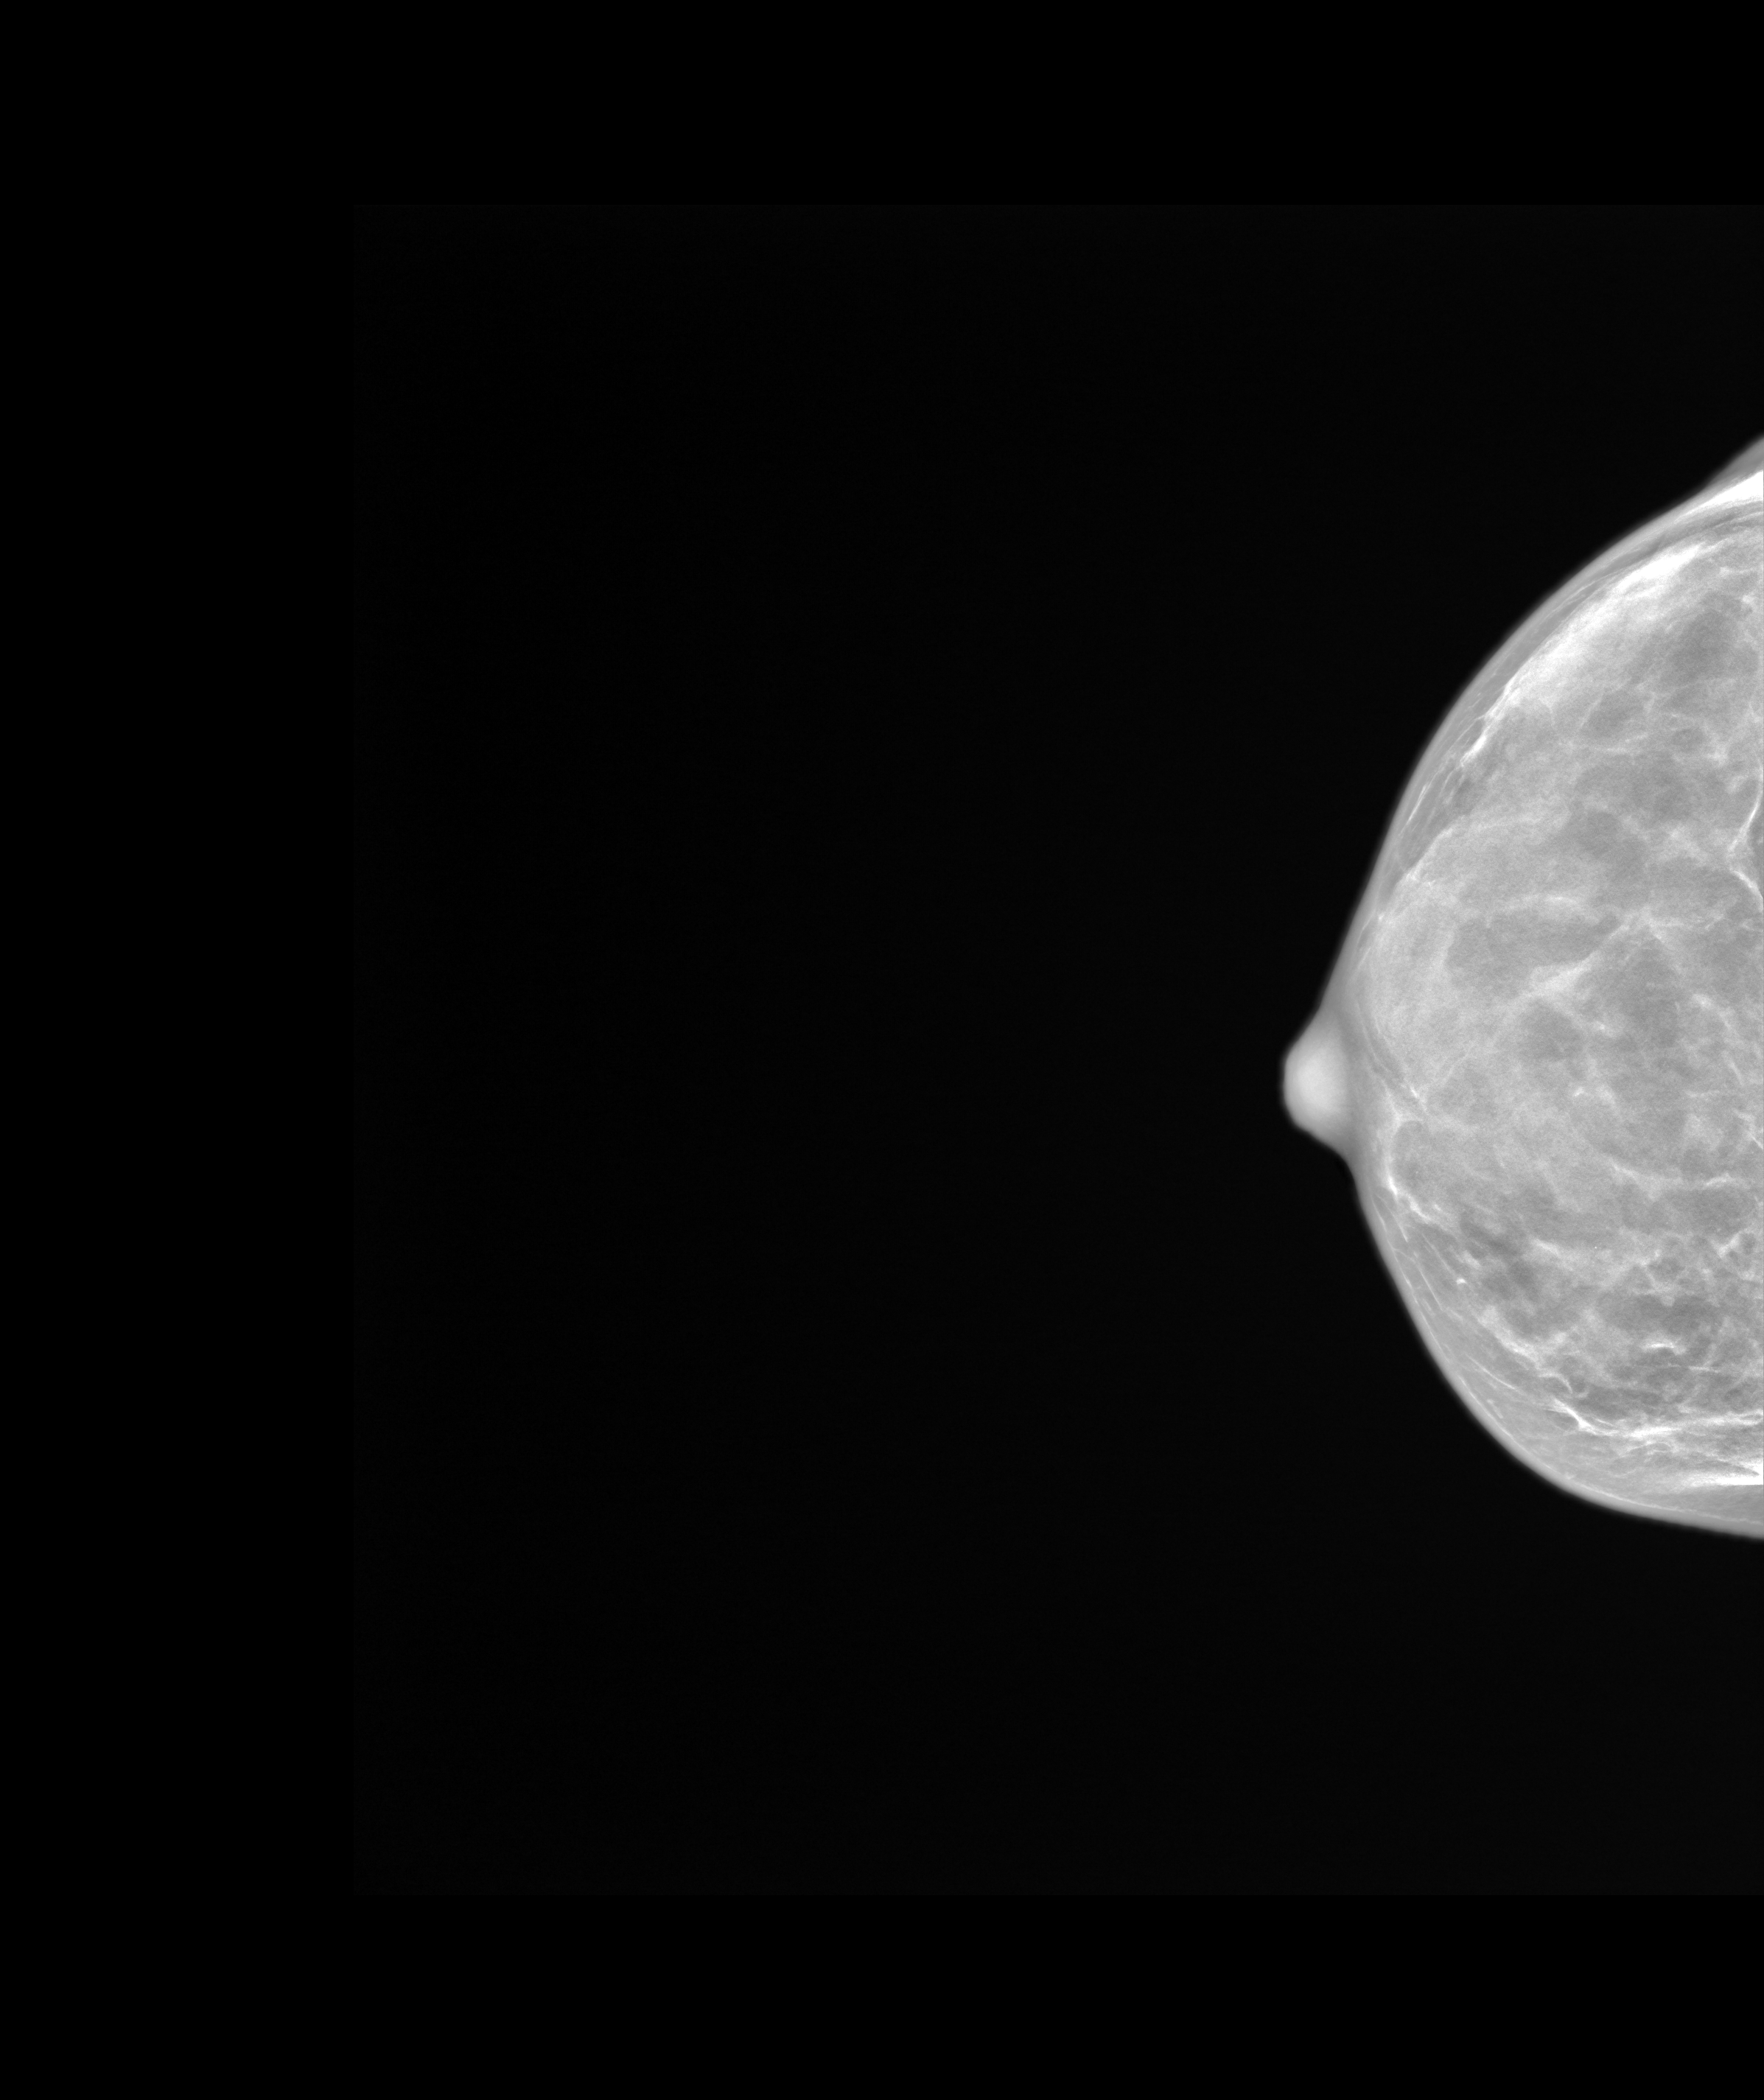
Screening examination. Female patient, age 55 years.
Image type: synthesized 2-D view from tomosynthesis. Breast: right. Projection: craniocaudal (CC) view.